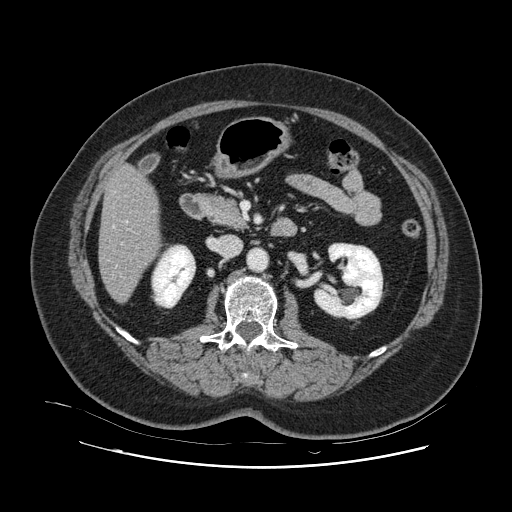
Contrast-enhanced abdominal CT, one axial slice. Slice 35 of 132 in the series (ordered by position). 120 kVp. Intravenous contrast given. Soft-tissue window (W 400 / L 40 HU). 2.5 mm slice thickness. 512 × 512 image matrix, field of view 391 × 391 mm. Female patient, age 73 years. Case-level facts recorded for this patient, not image findings: diagnosis: colorectal cancer liver metastases, imaged before liver resection; multiple liver metastases: no; largest metastasis: 7 cm; disease in both lobes: no.
Outlined on this slice (expert manual segmentation):
- hepatic veins: box from (x=113, y=225) to (x=117, y=267) px
- liver: (x=100, y=166)–(x=159, y=302)
- planned liver remnant (the part of the liver to remain after resection): (x=100, y=166)–(x=159, y=302)
- portal vein (with intrahepatic branches): (x=126, y=221)–(x=128, y=223)